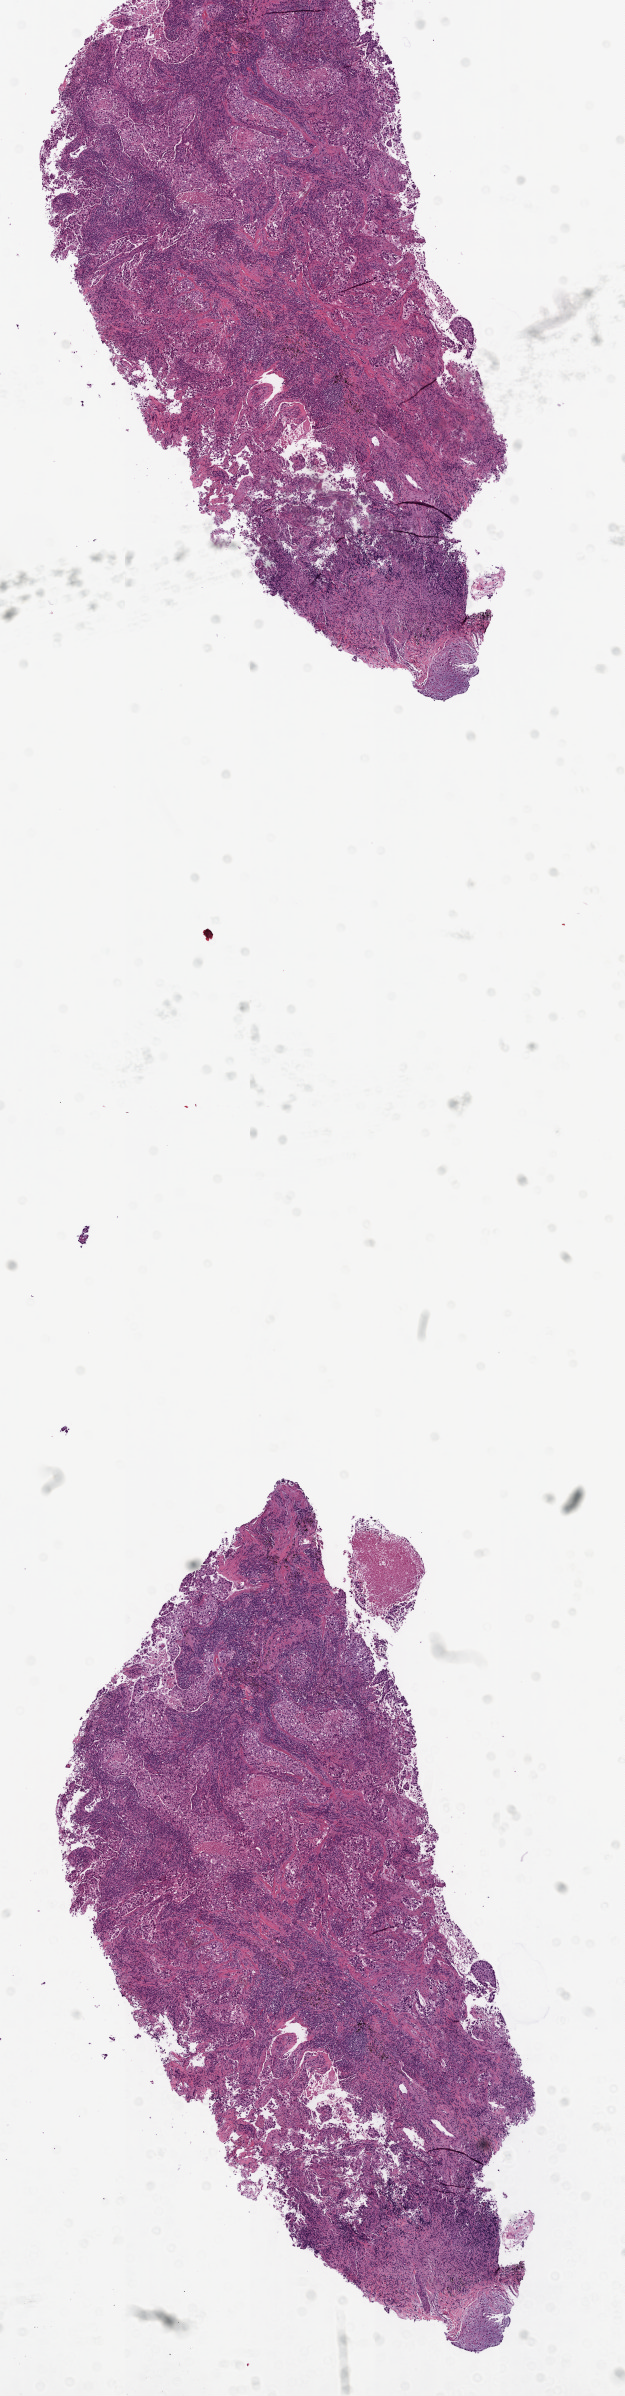
Digitized Hematoxylin and eosin (H&E) stained tissue section (whole slide) — shown as a low-resolution overview of the whole scanned area (about 5.0 x 19.2 mm); frozen section; lung, primary tumour sample. Female, age 62 years at initial diagnosis. Pathologist review of this section (percent, as recorded): tumour cells 70%, tumour nuclei 45%, normal cells 0%, stromal cells 25%, necrosis 5%. Inflammatory infiltration, as recorded: lymphocyte infiltration 35%.
AJCC pathologic stage: IIIA. Laterality: left. Histologic diagnosis: Squamous cell carcinoma, NOS (upper lobe, lung).